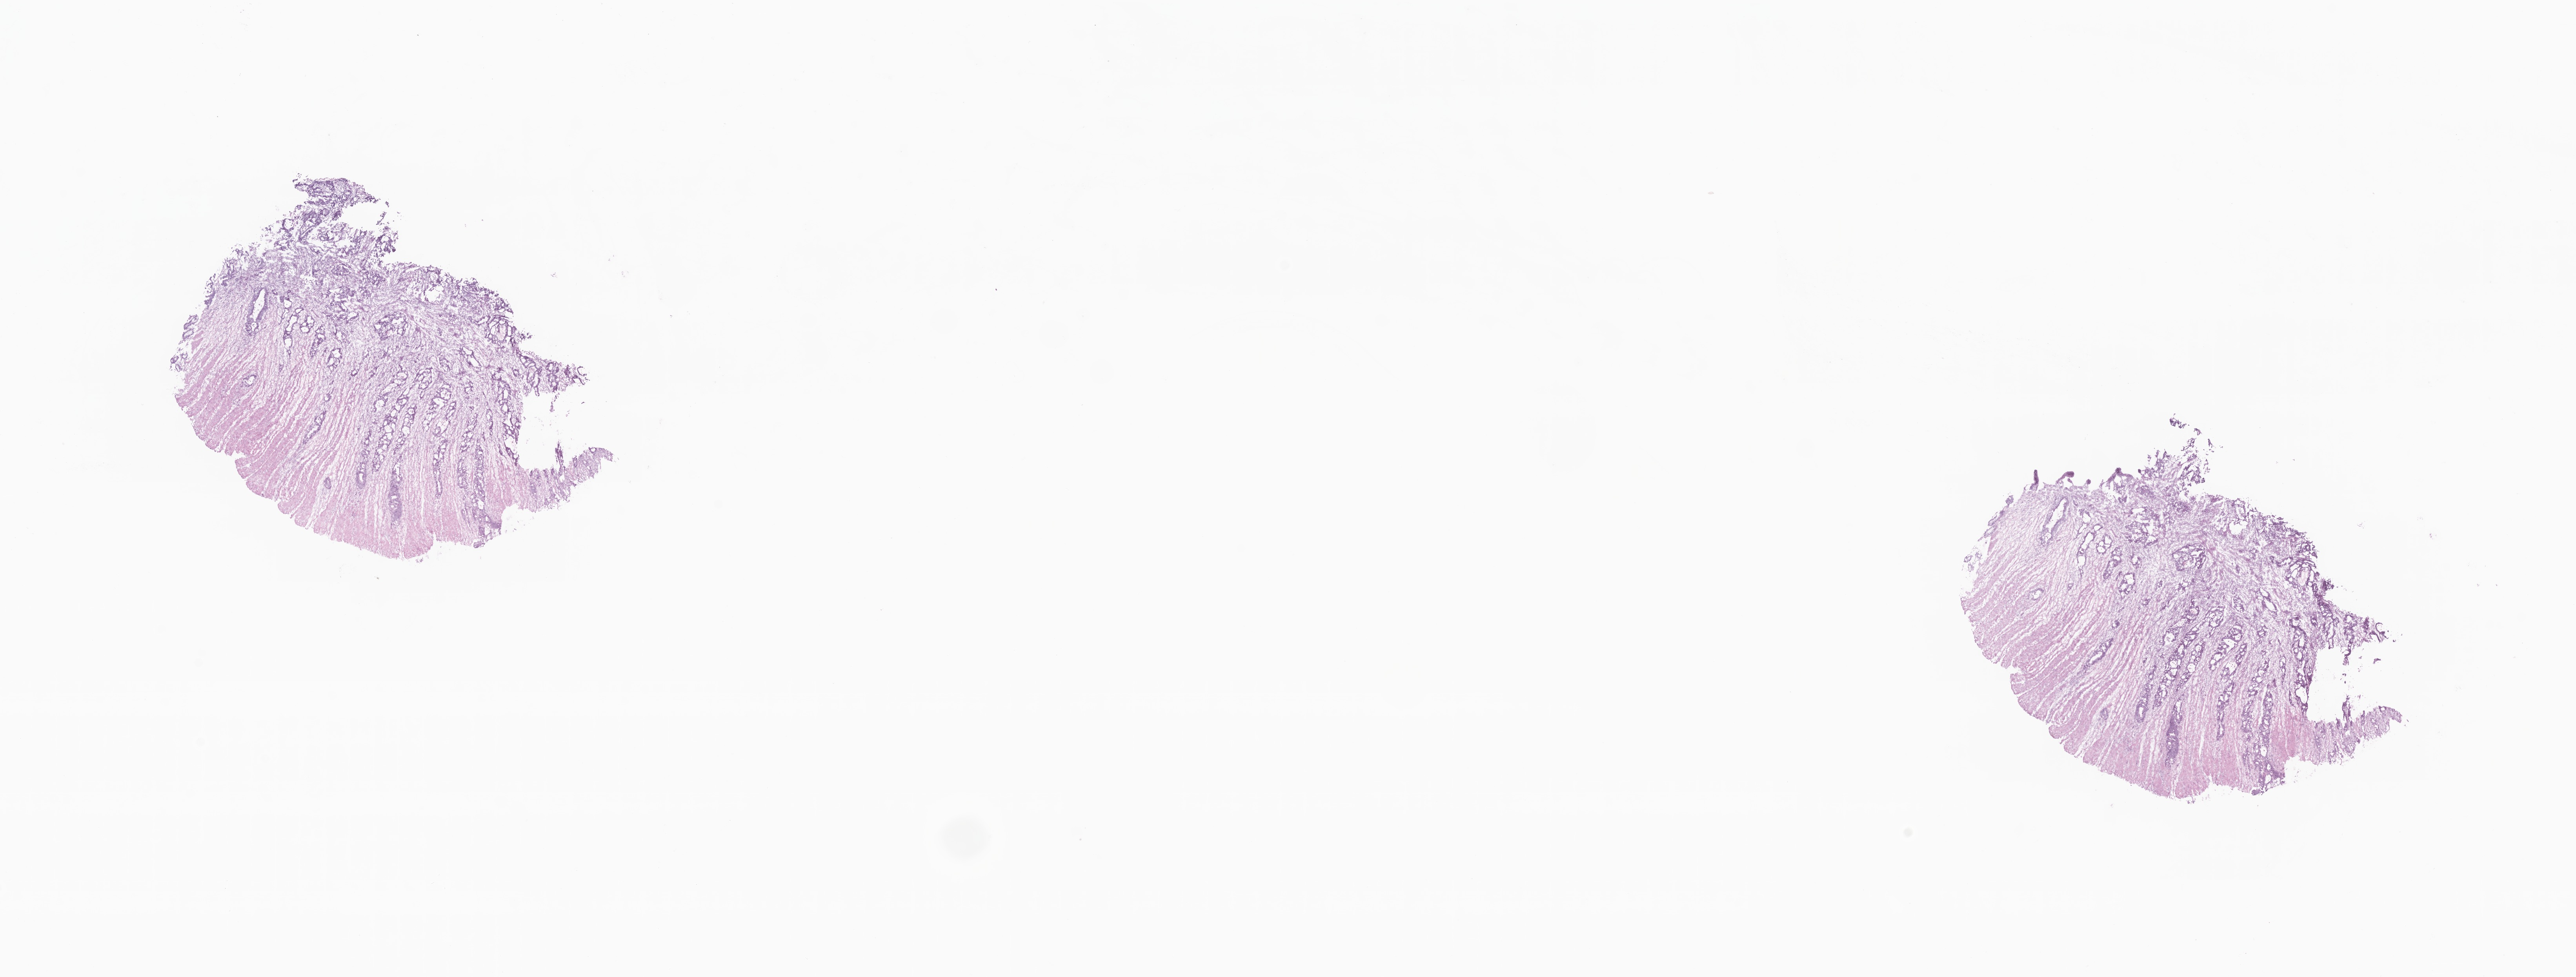
H&E whole-slide image, a low-resolution overview of the entire scanned area, about 27.7 x 10.5 mm, cryosection, primary tumor, anatomic site: sigmoid colon. Male patient; age at initial diagnosis 75 years. Slide review estimates, as recorded: tumor cells 40%, tumor nuclei 80%, stromal cells 60%, necrosis 0%, normal cells 0%. Inflammatory infiltration, as recorded: lymphocyte infiltration 50%, monocyte infiltration 0%, neutrophil infiltration 0%.
Section: top of the tissue portion. Histologic diagnosis: Adenocarcinoma, NOS.